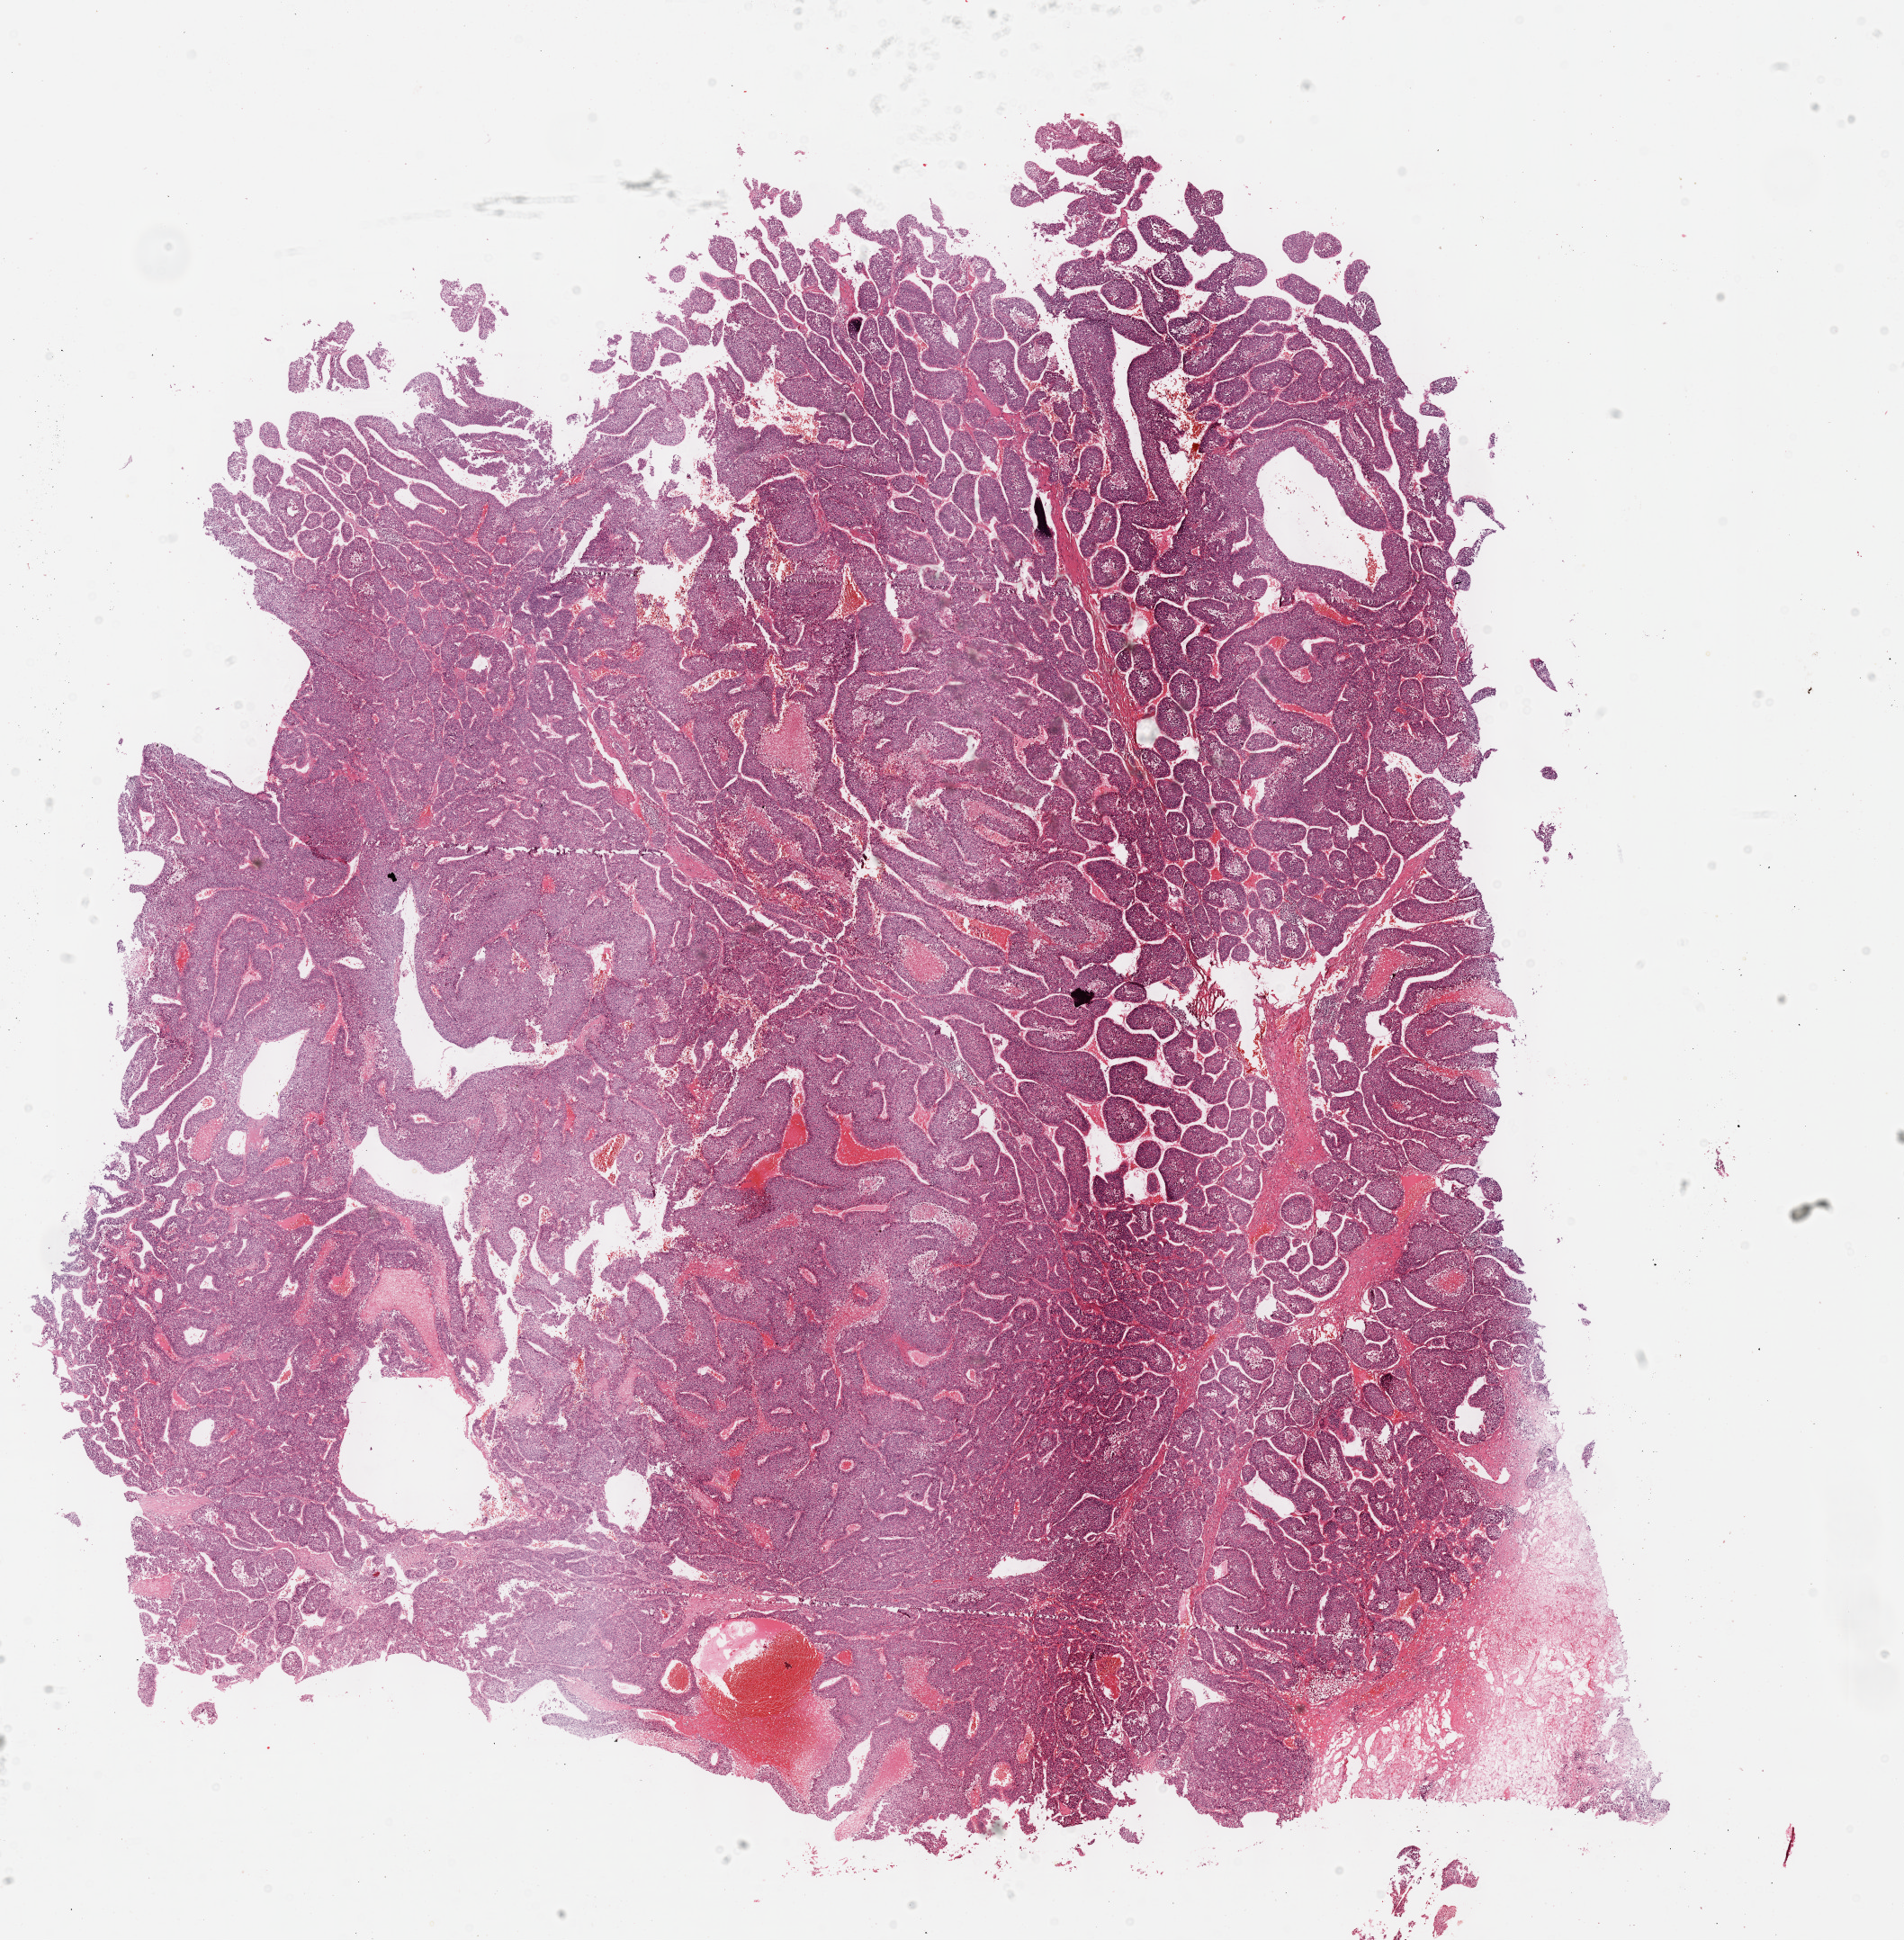
Digitized H&E-stained tissue section (whole slide) — a low-resolution overview of the entire scanned area, about 17.1 x 17.4 mm. Formalin-fixed paraffin-embedded (FFPE) diagnostic section. Liver, primary tumour sample. Female patient; age at initial diagnosis 52 years. Histologic grade: G2 (moderately differentiated).
- AJCC pathologic stage: IIIA
- TNM: T3a N0 M0
- histologic diagnosis: Hepatocellular carcinoma, NOS